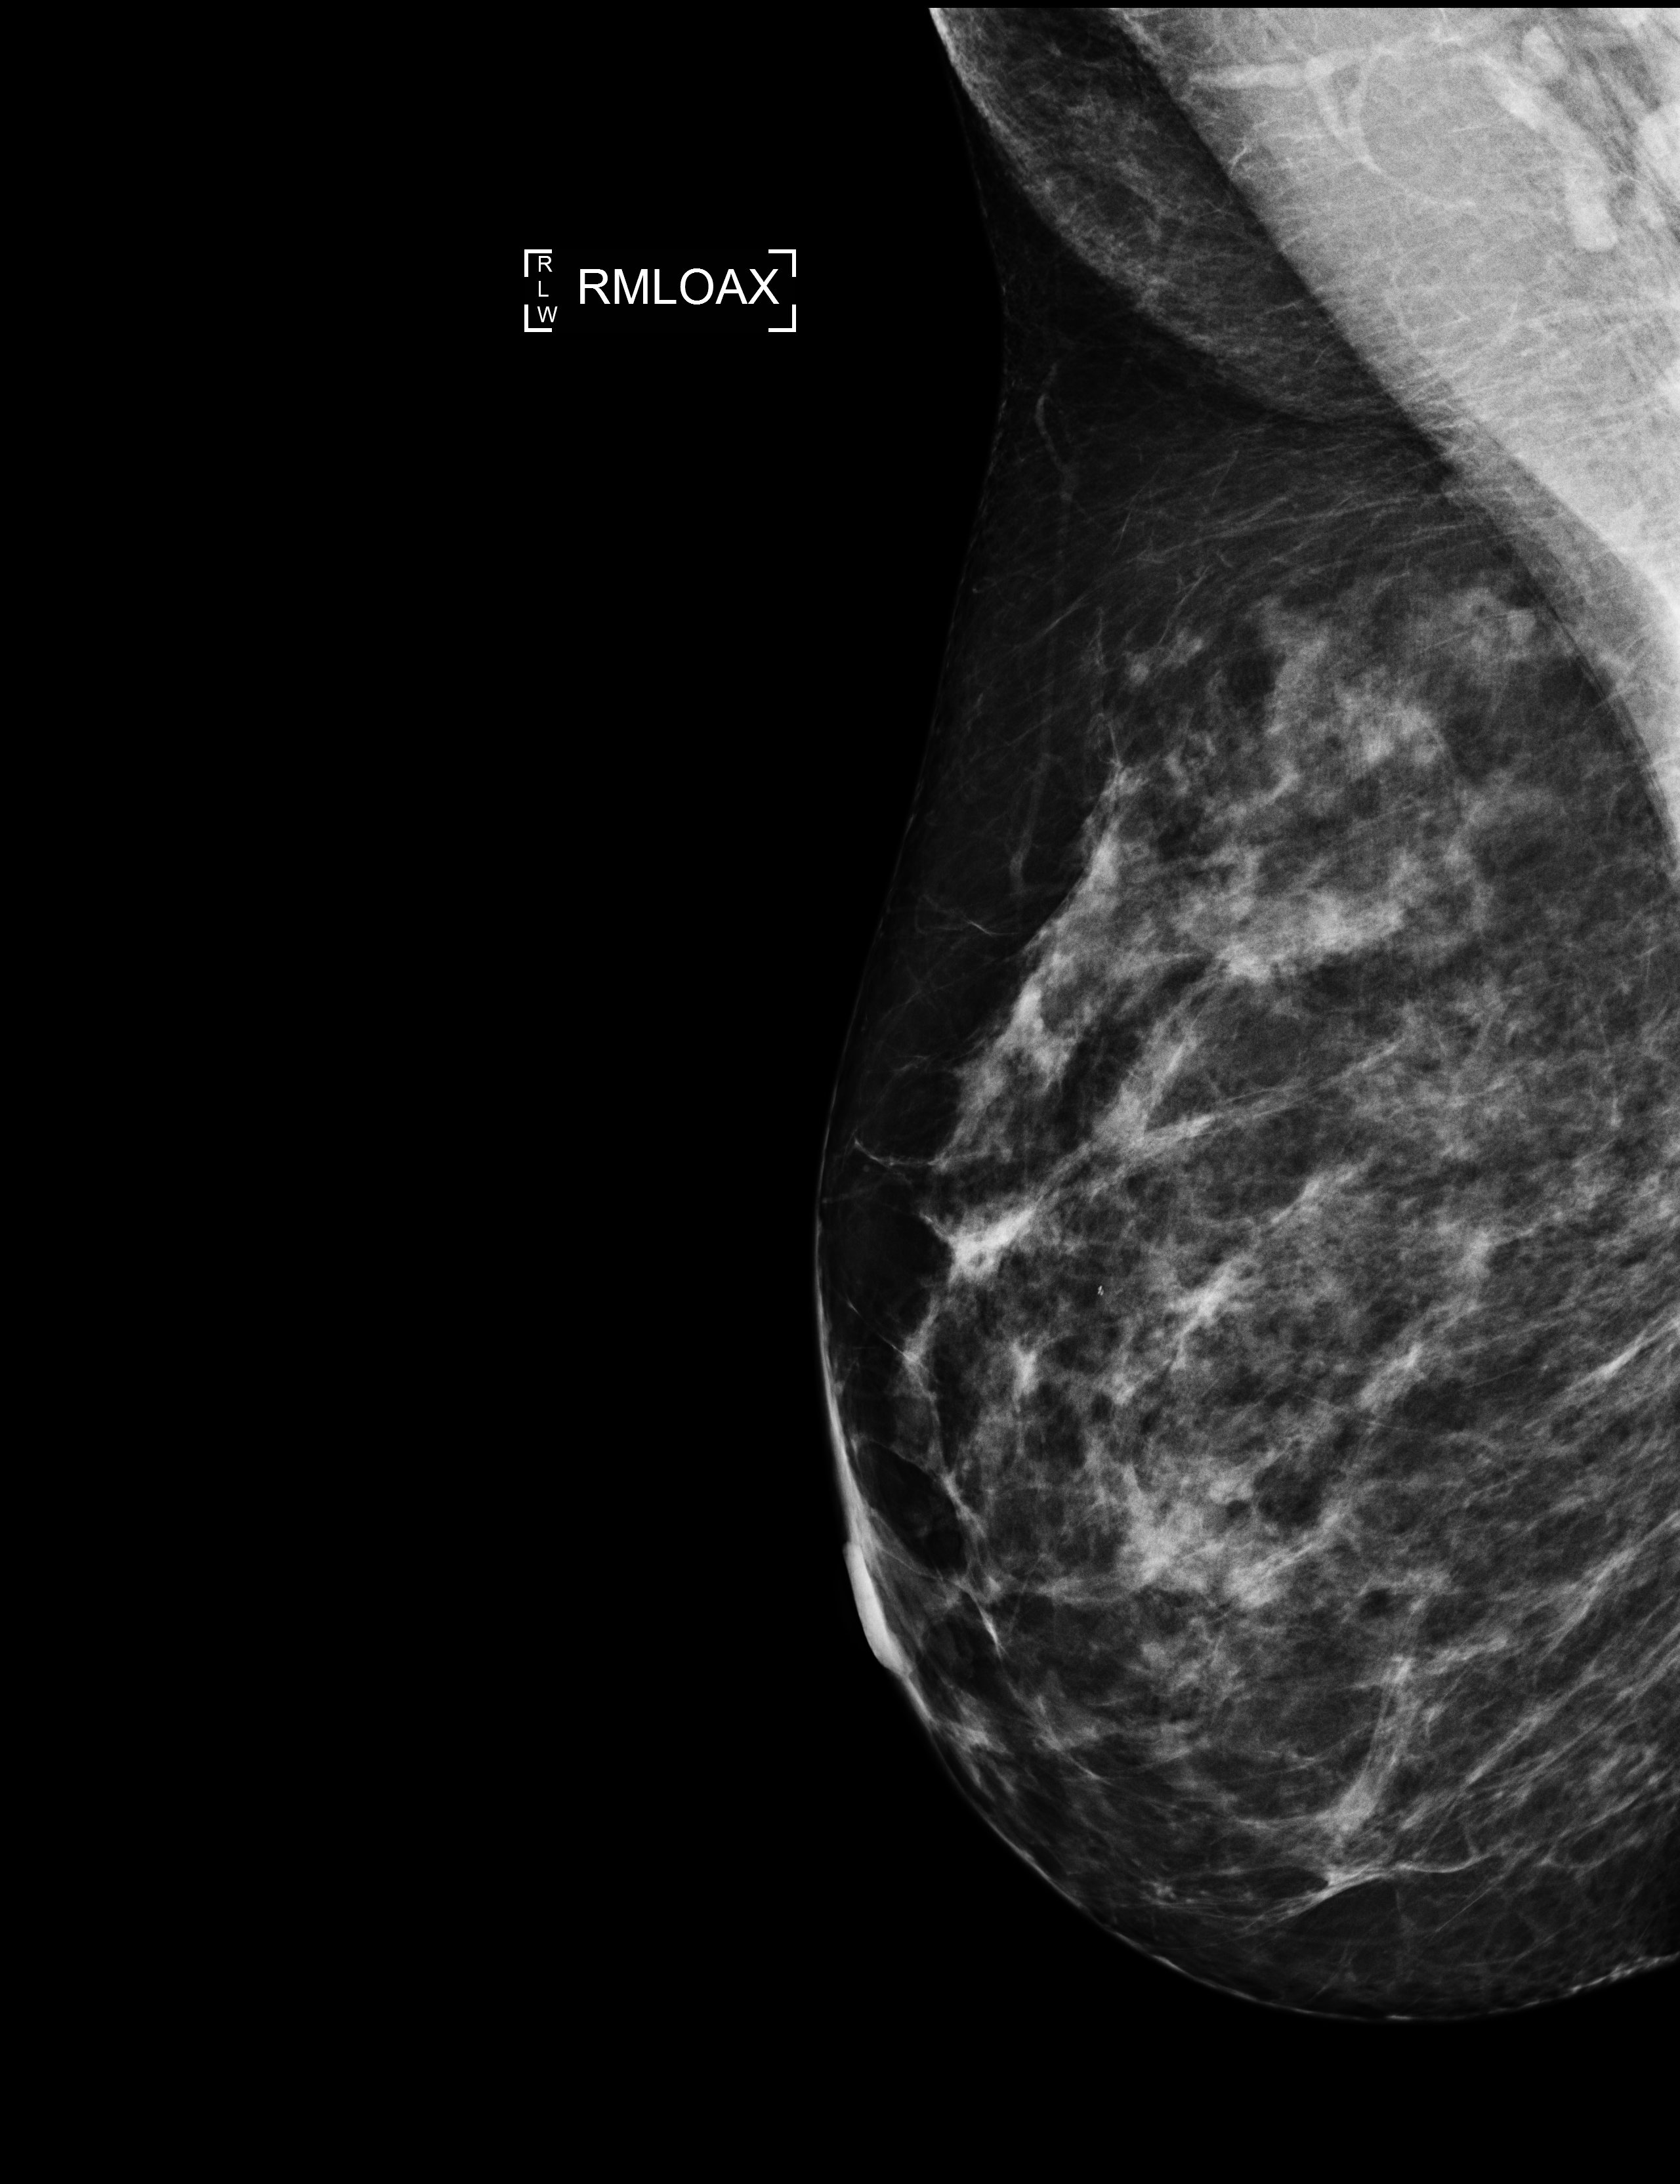
Digital mammogram (FFDM); right breast; mediolateral oblique (MLO) view (axillary tissue); annual screening mammography examination; compressed breast thickness 73 mm; system: Selenia Dimensions. Patient aged 48 years (female).
Breast density at the screening exam (both breasts): heterogeneously dense (BI-RADS density category c). Final BI-RADS category for the screening round (tomosynthesis exam, both breasts): category 1. Recall: no recall after this screen.